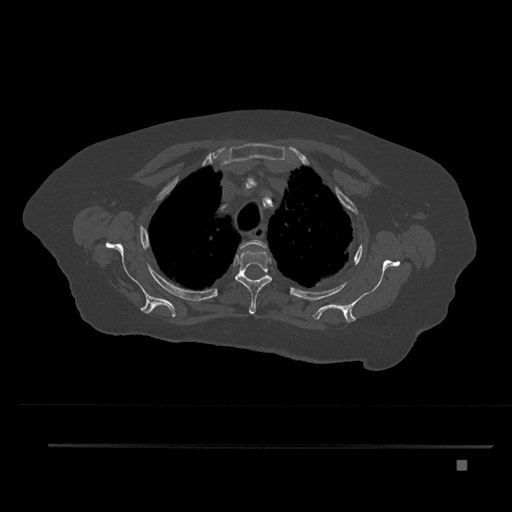
CT including the spine, one axial slice; position 636 of 797 along the scan axis; reconstruction kernel Br40s/3; 120 kVp; bone window (W 1800 / L 400 HU); 0.5 mm slice thickness; 512 × 512 image matrix. Patient: female, 76 years. From the clinical record (not read from this slice): primary cancer: lung.
Annotated regions visible in this slice (semi-automatic segmentation, software-assisted and operator-edited):
- T2 vertebra: bounding box <240,240,267,249> (left, top, right, bottom; pixels)
- T3 vertebra: <235,251,272,315>